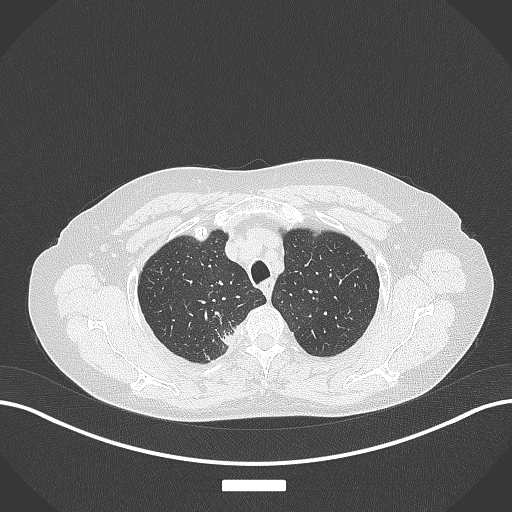
Chest CT, one axial slice. Position 325 of 357 along the scan axis. Reconstruction kernel B70f. 120 kVp. Lung window (W 1500 / L -600 HU). 512 × 512 image matrix, field of view 400 × 400 mm. Patient: female, 62 years. From the clinical record (not read from this slice): clinical TNM (as recorded): T1c N1 M0.
Annotated regions visible in this slice (bounding box drawn by a radiologist):
- lung tumour (recorded histology: squamous cell carcinoma): bounding box (x1, y1, x2, y2) in pixels: (215, 330, 240, 356)